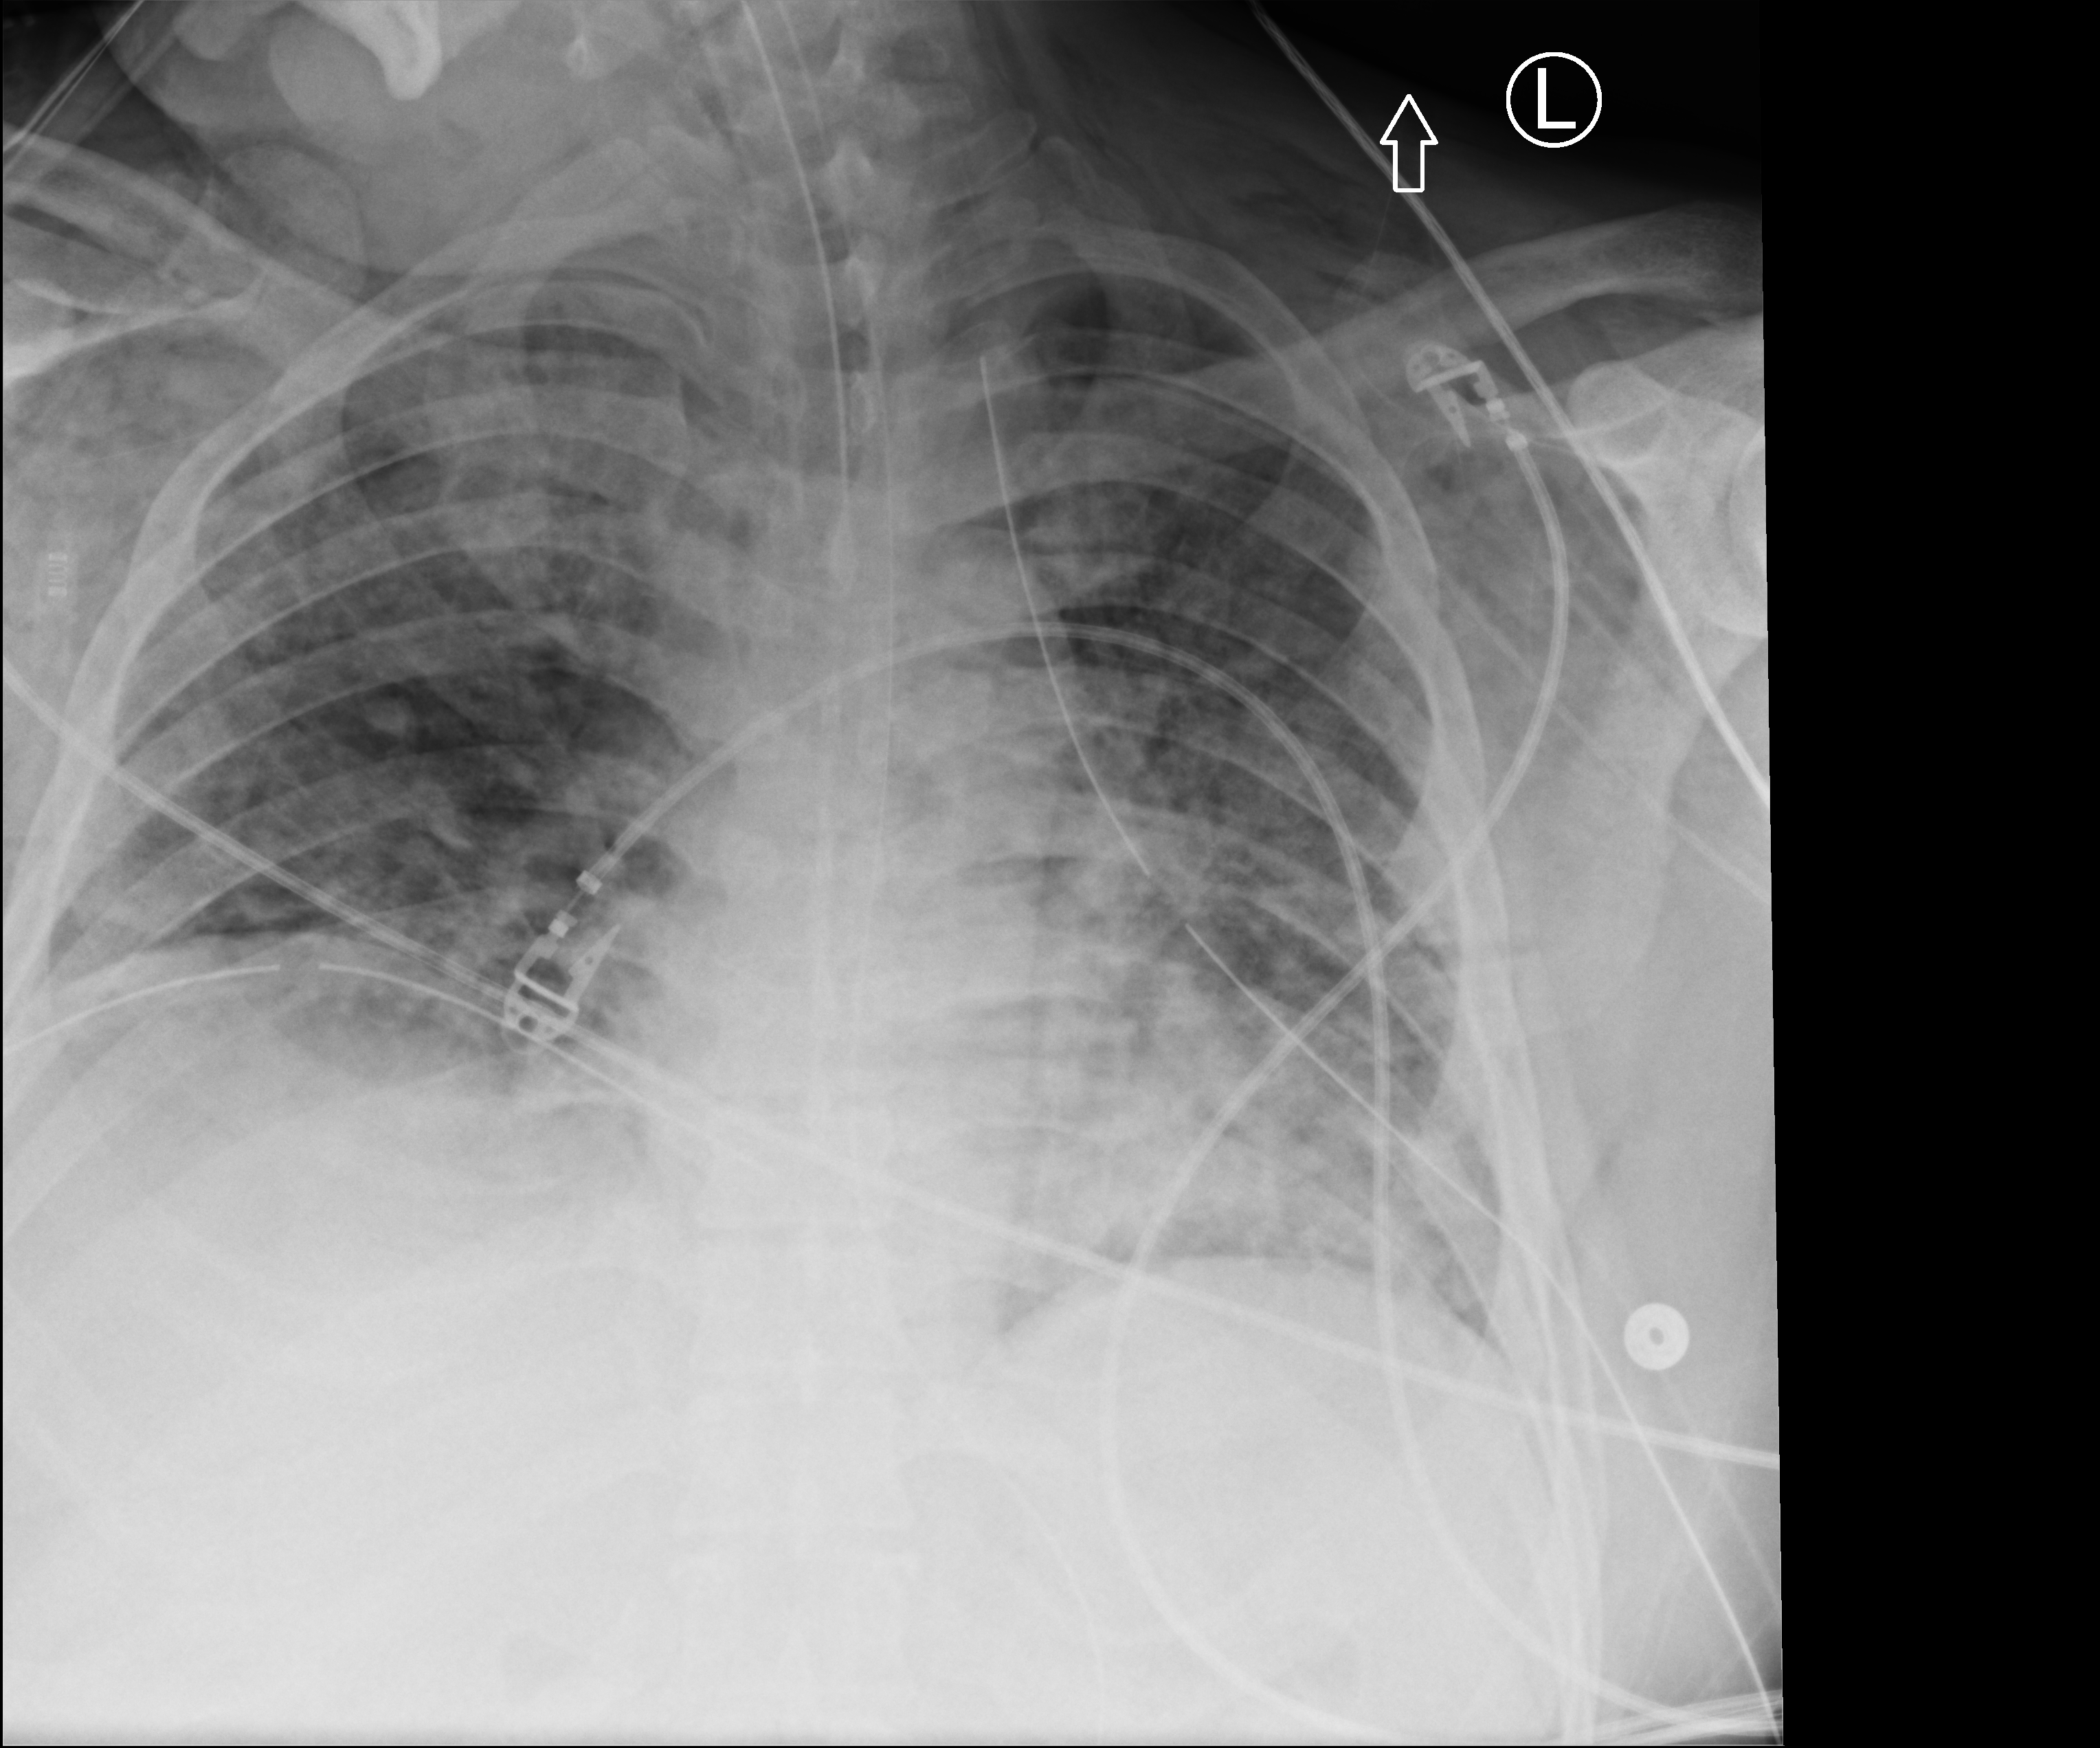
Bedside chest radiograph (computed radiography), anteroposterior (AP) projection. Male patient hospitalised with COVID-19, age 18–59 years.
Admission-level facts for this patient (not findings on this image; timing relative to this image not recorded): admitted to intensive care during this hospital stay: yes.